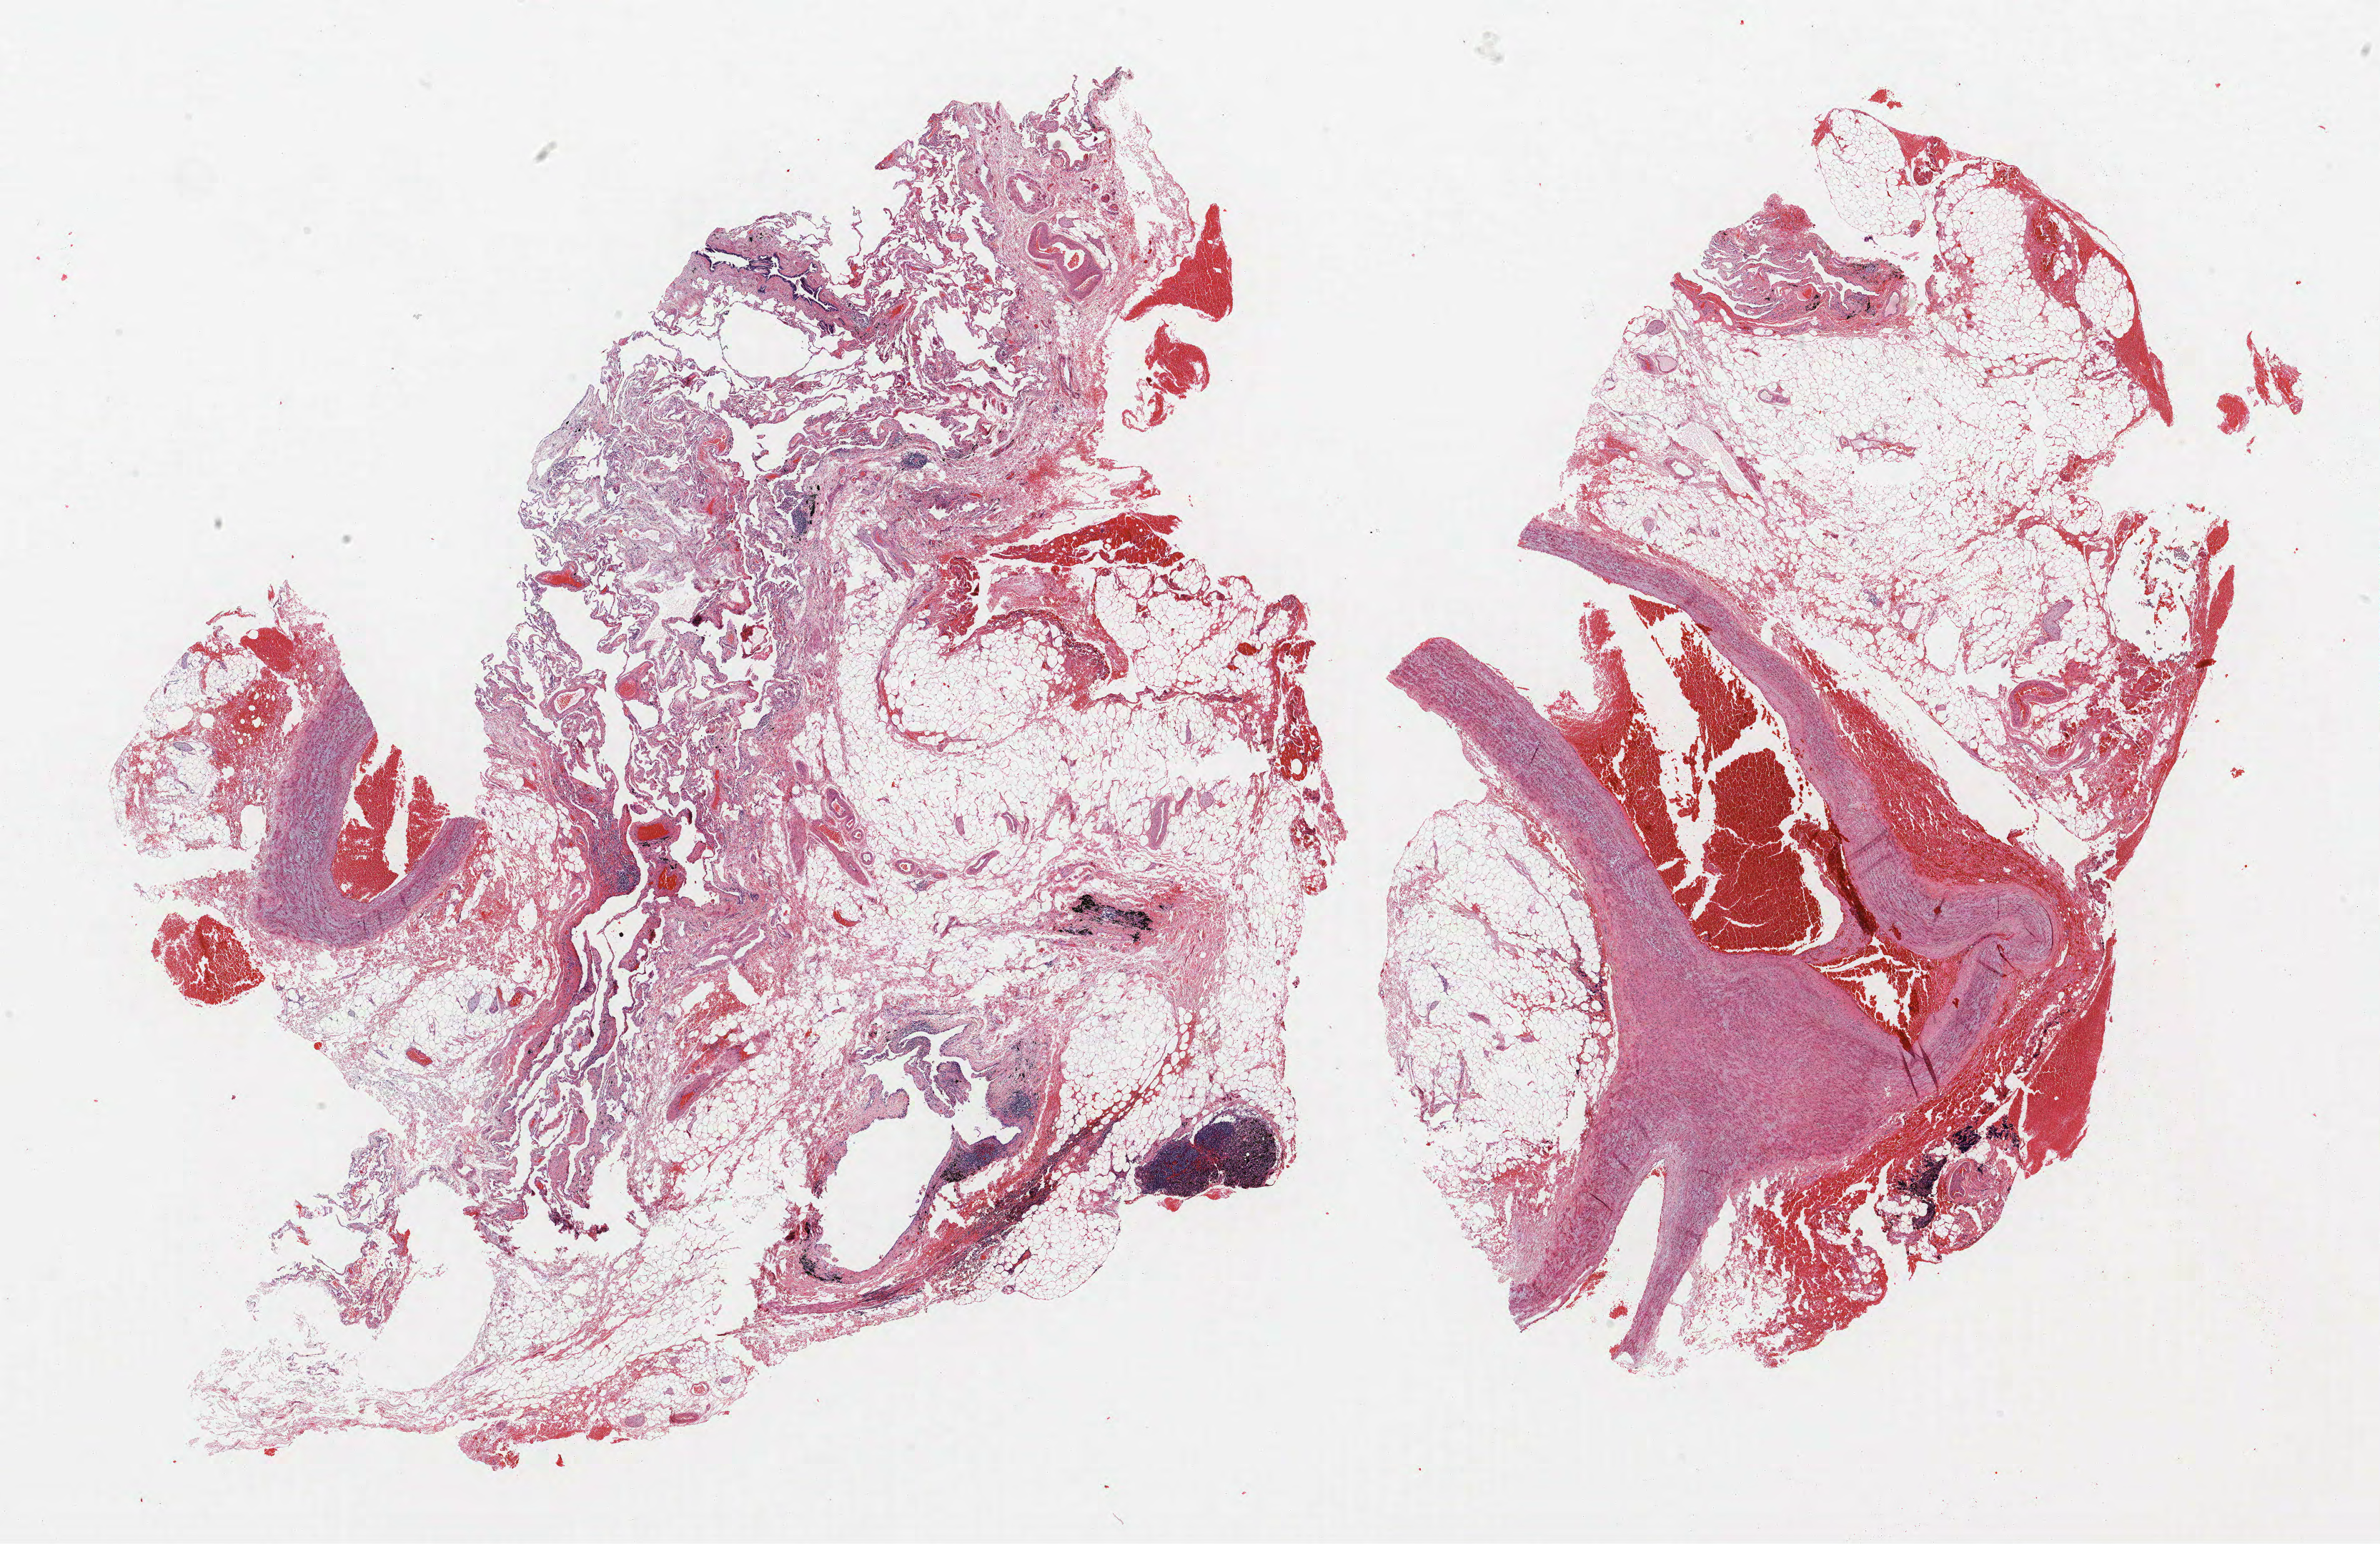
Whole-slide histology image, H&E — a low-resolution overview of the entire scanned area, about 26.6 x 17.3 mm (acquisition: 40x scan). Formalin-fixed paraffin-embedded (FFPE) section. Lung tissue. Male patient, aged 65 at enrolment. Former smoker at enrolment. Grade: moderately differentiated (G2).
Primary tumour location (clinical record): right upper lobe. Stage (AJCC 6th edition): IIA. Participant's lung-cancer diagnosis: Bronchiolo-alveolar adenocarcinoma, NOS (ICD-O-3 8250/3). Tumour size (pathology): 14 mm.